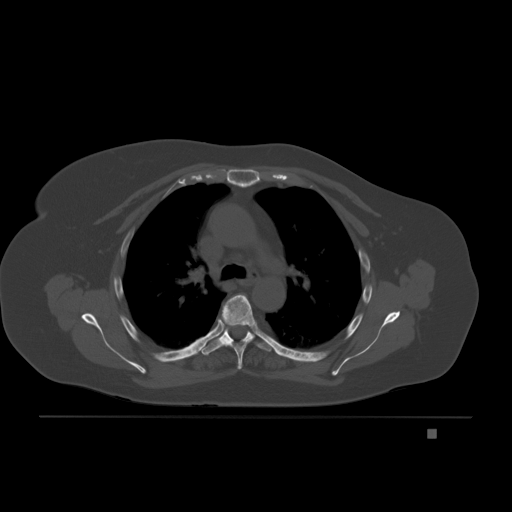
CT including the spine, one axial slice; slice 149 of 221 in the series (ordered by position); bone window (W 1800 / L 400 HU); 512 × 512 image matrix. Female patient, age 63 years. Case-level facts recorded for this patient, not image findings: primary cancer: breast.
Annotated regions visible in this slice (semi-automatic segmentation, software-assisted and operator-edited):
- T4 vertebra: bounding box (x1, y1, x2, y2) in pixels: (222, 294, 253, 370)
- T5 vertebra: (201, 327, 272, 356)